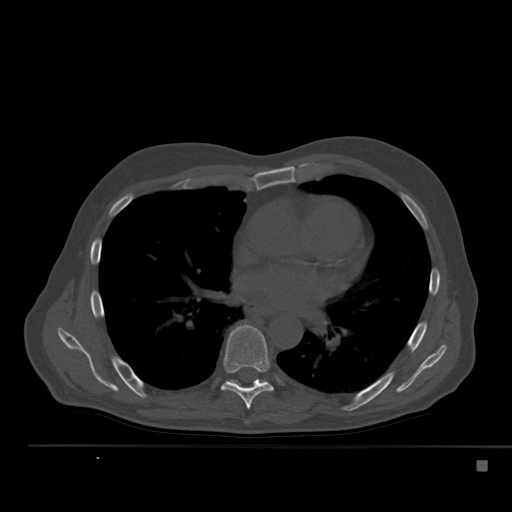
CT including the spine, one axial slice; position 325 of 517 along the scan axis; 120 kVp; bone window (W 1800 / L 400 HU); 1.5 mm slice thickness; 512 × 512 image matrix, field of view 408 × 408 mm. Male patient, age 70 years. From the clinical record (not read from this slice): primary cancer: renal; vertebrae with lytic lesions (as recorded): T4, T6, T10, T12, L3, L4, L5.
Structures marked on this image (semi-automatically segmented with operator editing):
- T7 vertebra: bounding box <221,325,273,409> (left, top, right, bottom; pixels)